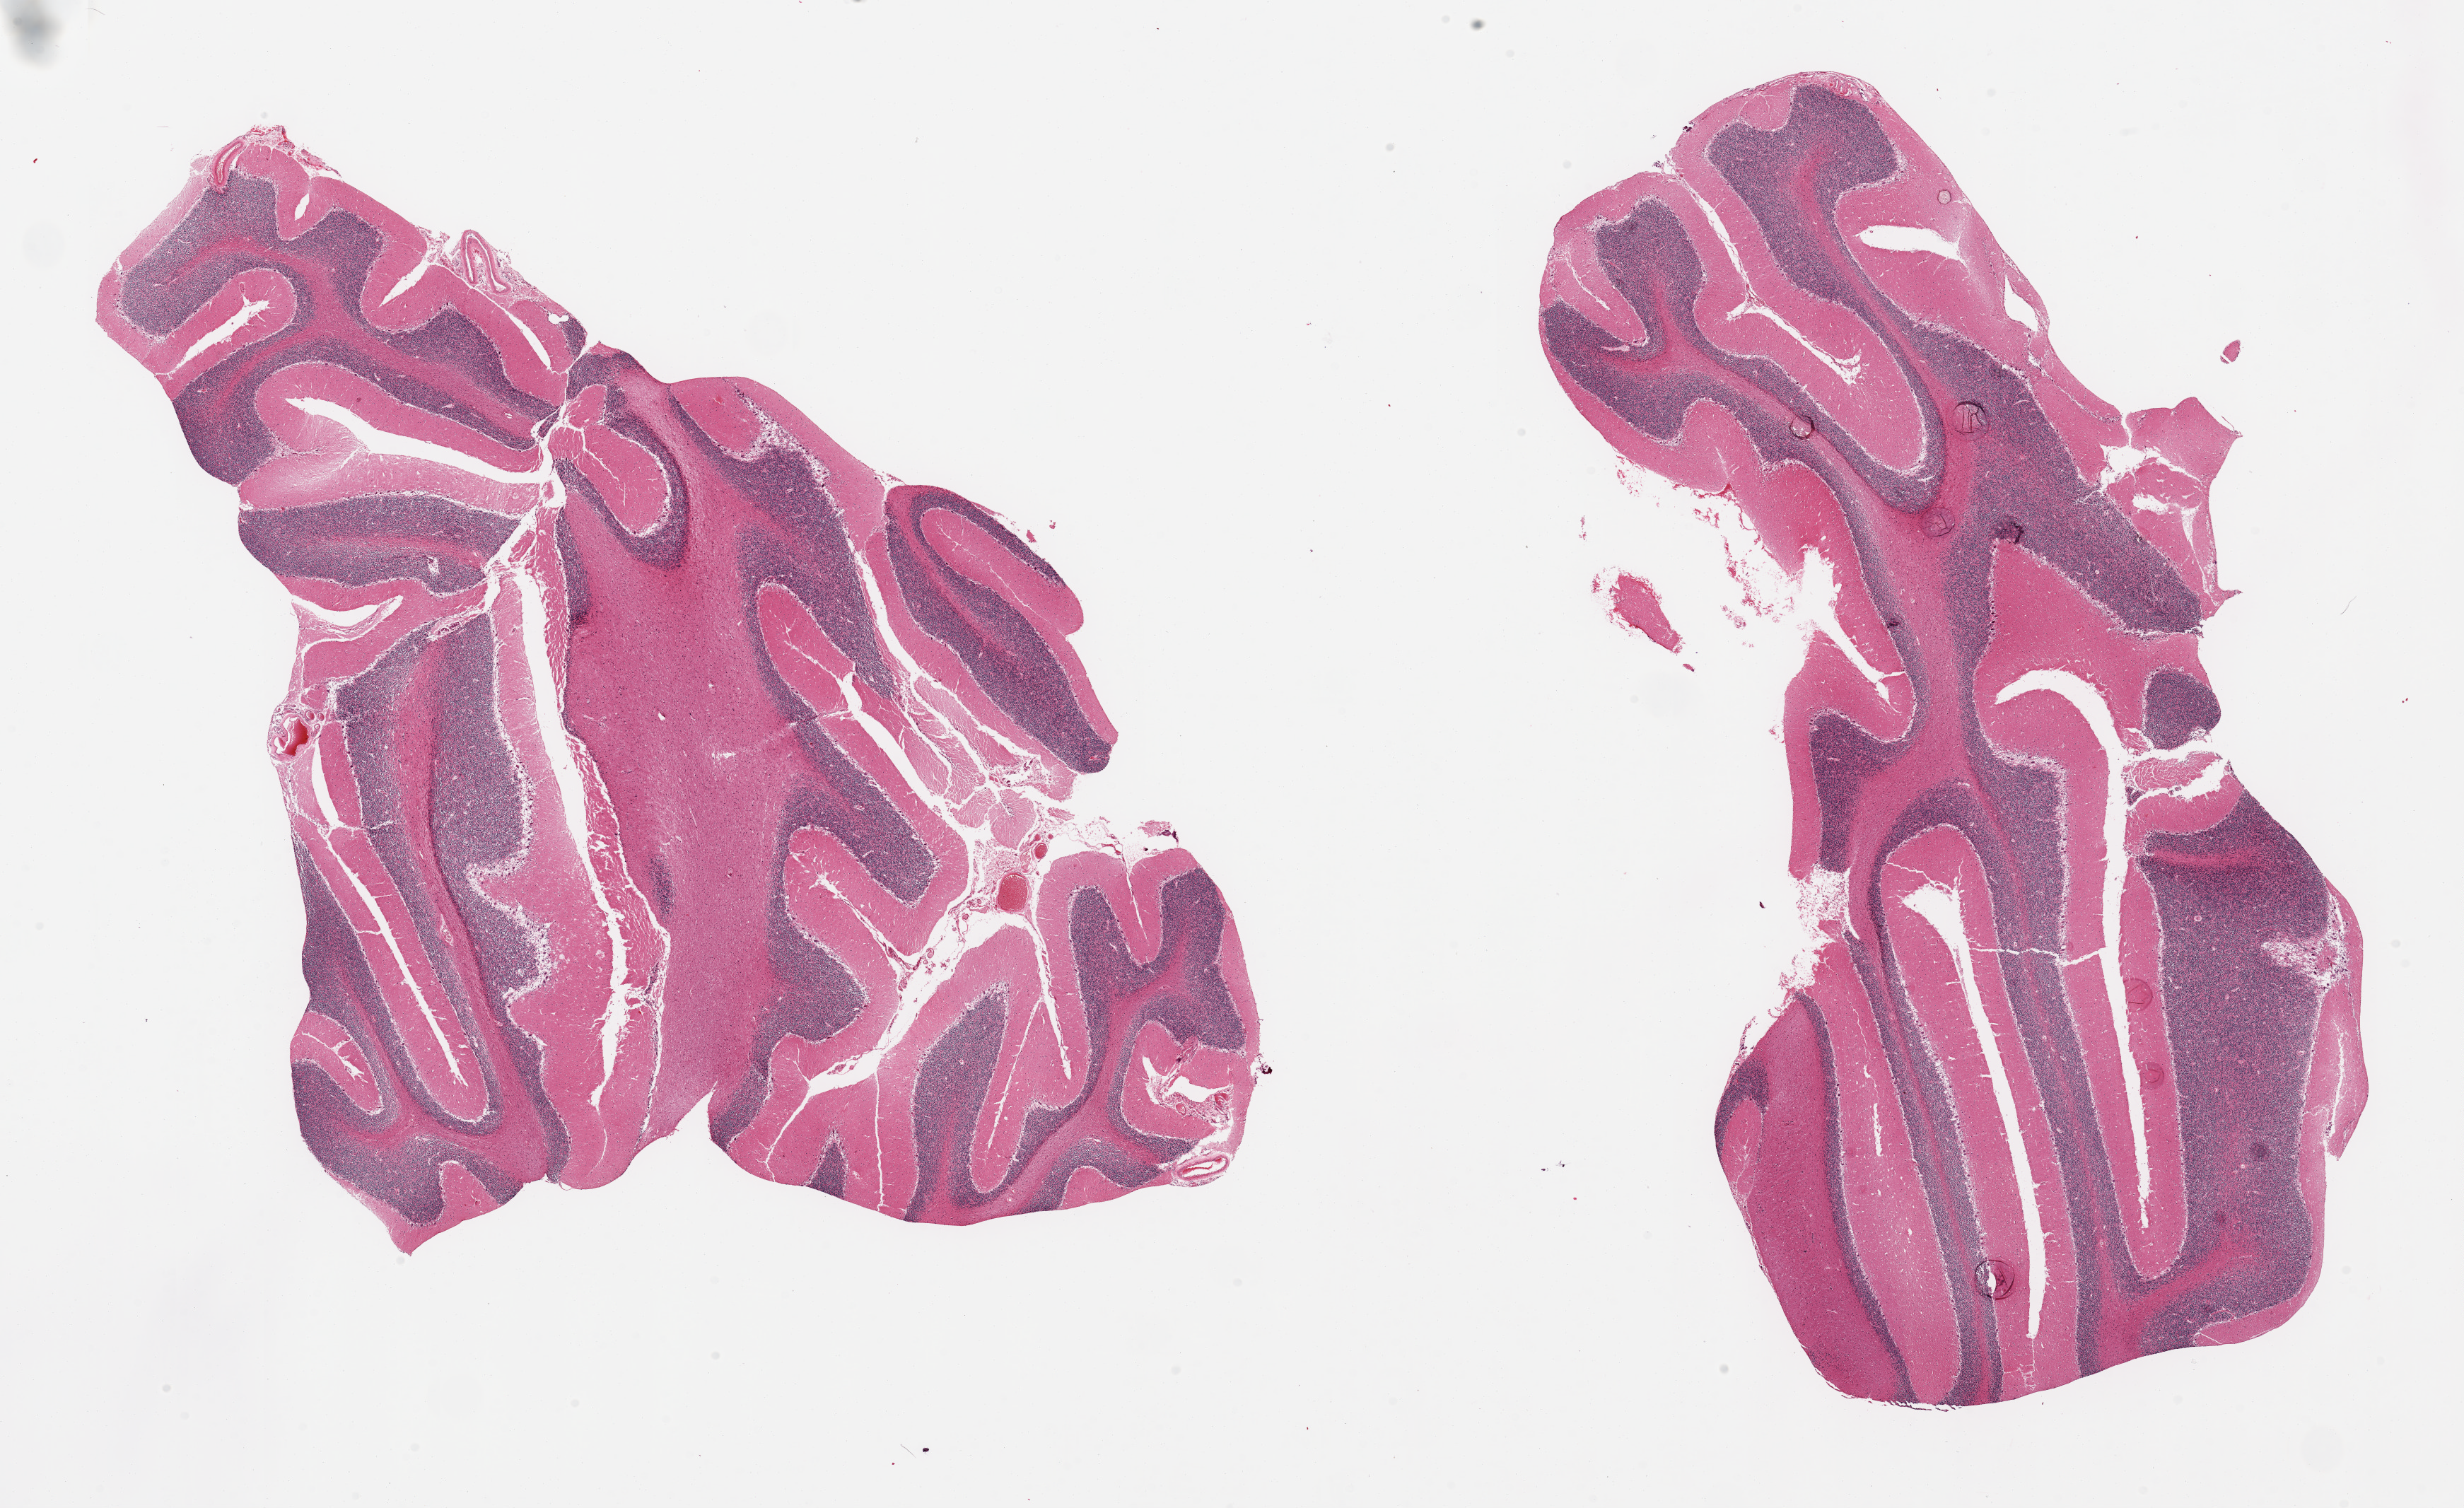
Whole-slide image, hematoxylin and eosin (H&E) stain, low-resolution overview of the scanned area, about 27.6 x 16.9 mm (acquisition: 20x scan), PAXgene-fixed paraffin-embedded (PFPE) section, section of cerebellum (target tissue), tissue donor sample. Donor: male.
• review note (as recorded): 2 pieces, no abnormalities